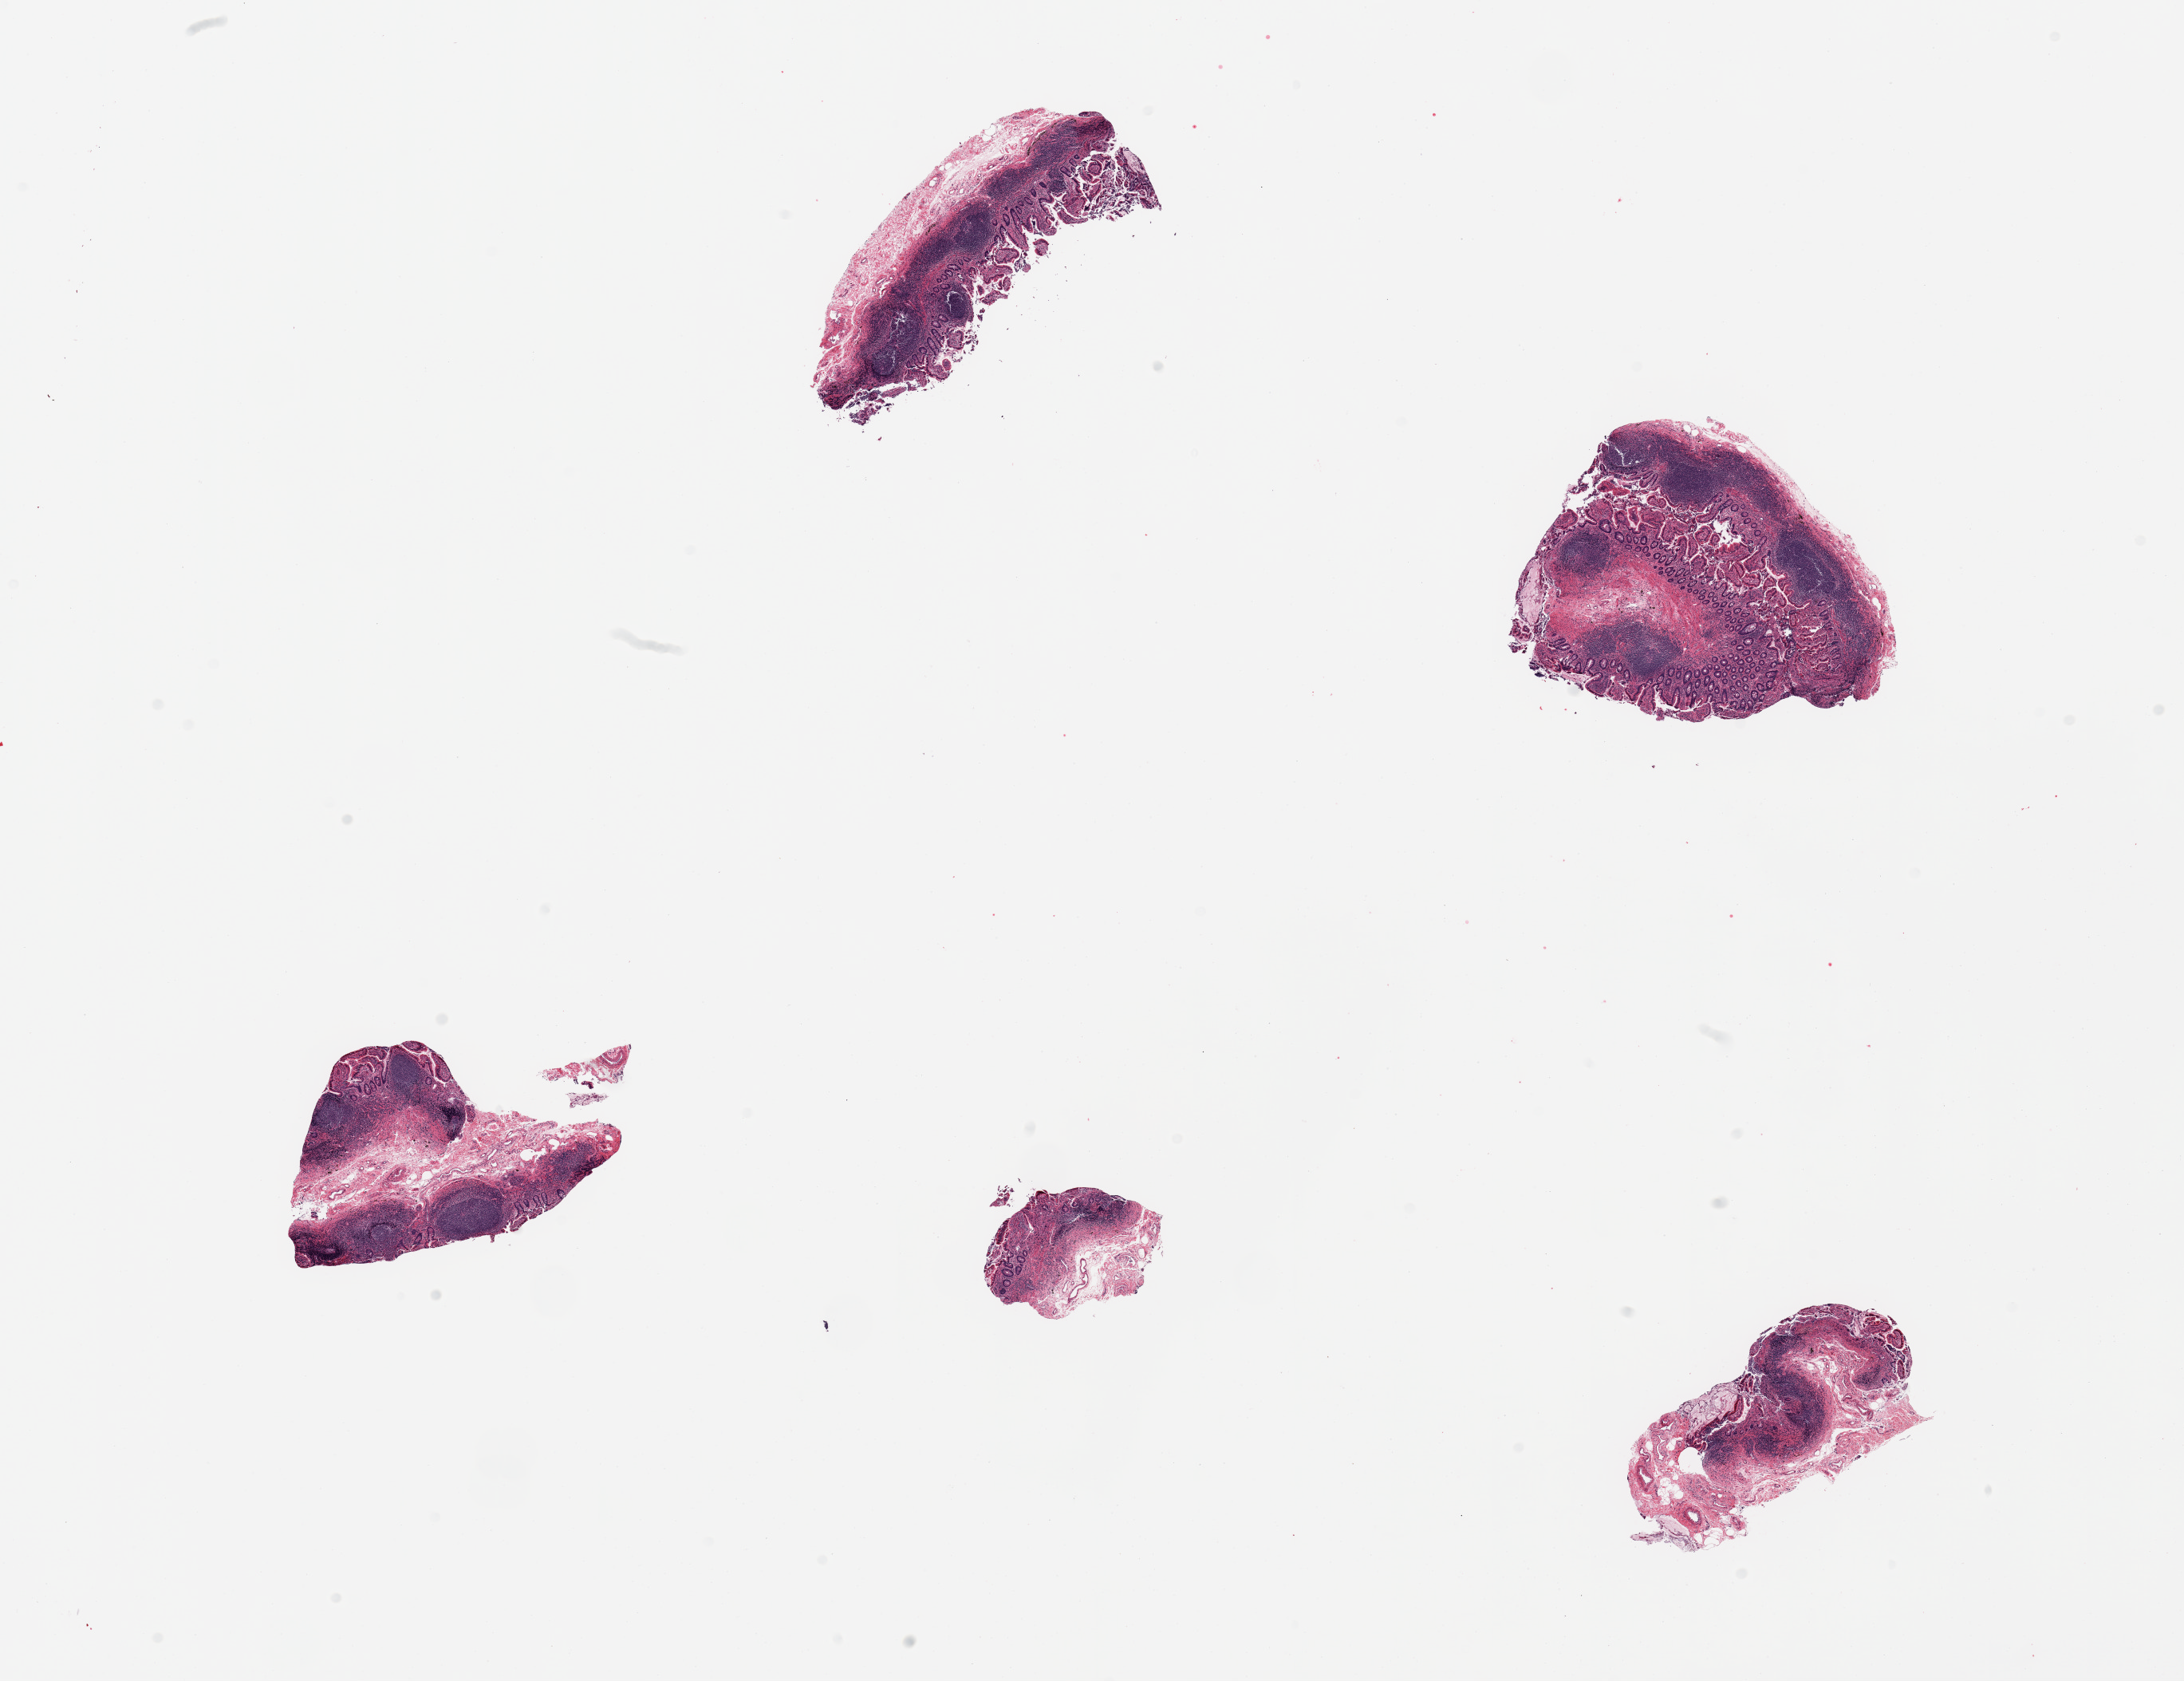
Whole-slide image, H&E stain, brightfield — whole scanned area (about 21.7 x 16.7 mm, slide scanned at 20x) shown as a low-resolution overview; PAXgene-fixed, paraffin-embedded tissue; section of ileum (target tissue); donor tissue sample. Donor: female.
Pathologist's review note for this sample: 5 pieces; excellent specimen, mucosa only with prominent lymphoid component.